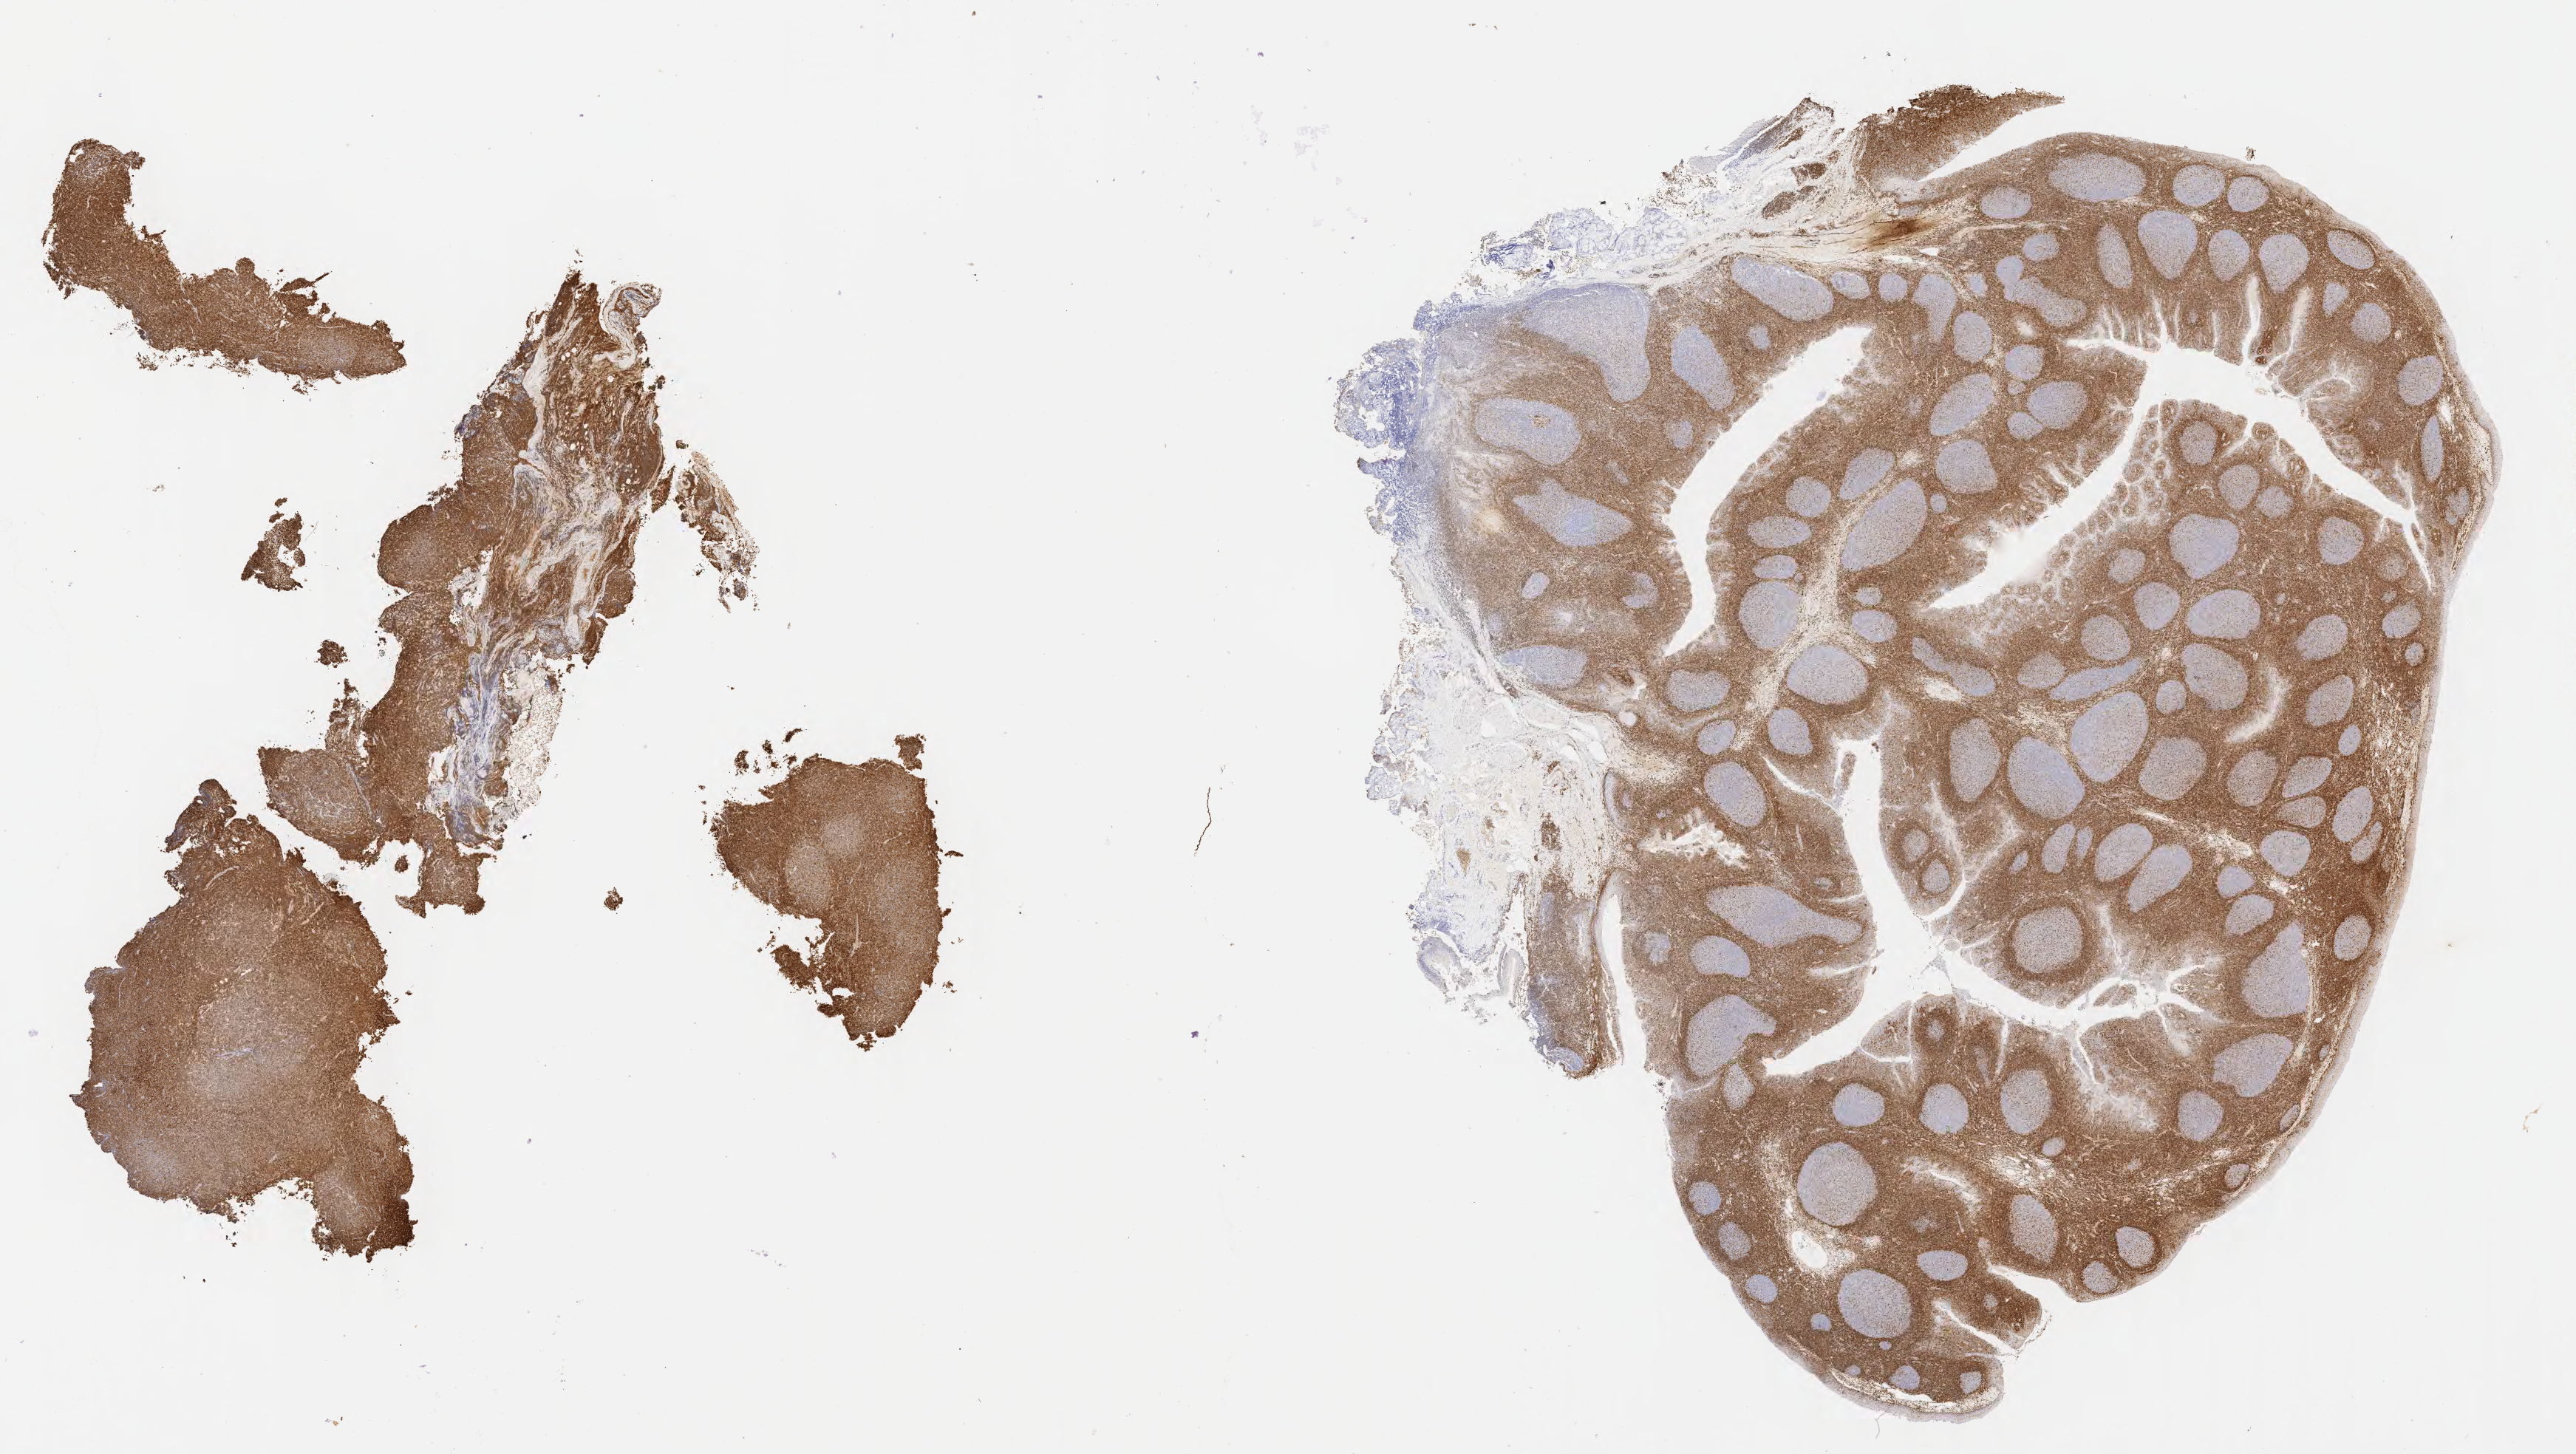
IHC for BCL2, whole-slide image — a low-resolution overview of the entire scanned area, about 28.2 x 15.9 mm. Tumor tissue. Site: liver. Patient: female, age 36 years.
Histologic diagnosis: Diffuse large B-cell lymphoma, NOS.